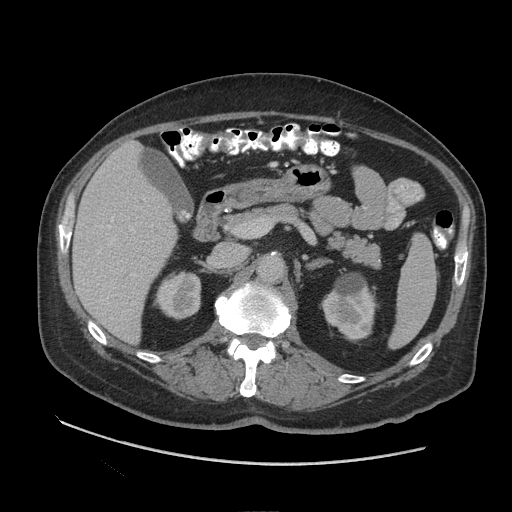
Contrast-enhanced abdominal CT (liver protocol), one axial slice; position 47 of 109 along the scan axis; reconstruction kernel STANDARD; 140 kVp; soft-tissue window (W 400 / L 40 HU); 2.5 mm slice thickness; 512 × 512 image matrix. From the clinical record (not read from this slice): diagnosis: hepatocellular carcinoma (patient treated with transarterial chemoembolisation; whether this scan precedes or follows treatment is not stated here); TNM stage (as recorded): Stage-I; Child-Pugh class: A; tumour nodularity: uninodular.
Outlined on this slice (semi-automatically segmented with operator editing):
- liver parenchyma outside the tumour (the mass and vessels are separate outlines, so this box may not span the whole liver): bounding box [x1, y1, x2, y2] px = [72, 140, 176, 342]
- liver vessels: [98, 216, 135, 276]